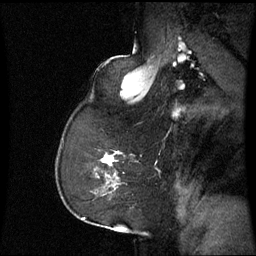
Breast MRI (dynamic contrast-enhanced), one sagittal slice. Position 43 of 60 along the scan axis. Dynamic contrast-enhanced series, image 2 of 3 at this slice position (ordered by acquisition). 1.5 T. TE 4.2 ms, TR 8.9 ms. 2.4 mm slice thickness. 256 × 256 image matrix, field of view 220 × 220 mm. Patient: female, 59 years. Case-level facts recorded for this patient, not image findings: setting: breast cancer imaged before/during neoadjuvant chemotherapy; receptor status: triple-negative.
Outlined on this slice (semi-automatic segmentation, software-assisted and operator-edited):
- analysis volume of interest (the breast-tissue region the enhancement analysis was run in; not a lesion): box from (x=96, y=152) to (x=125, y=197) px
- tumour enhancement mask (voxels above the 70 % enhancement threshold inside the analysis volume of interest): (x=102, y=156)–(x=113, y=165)